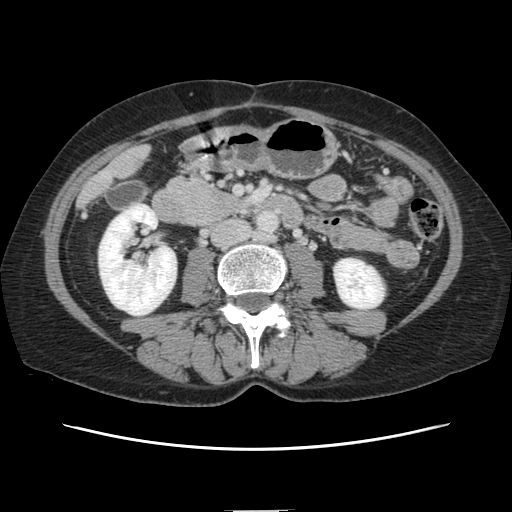
Contrast-enhanced abdominal CT, one axial slice. Slice 29 of 141 in the series (ordered by position). 120 kVp. Intravenous contrast given. Soft-tissue window (W 400 / L 40 HU). 2.5 mm slice thickness. 512 × 512 image matrix. Female patient, age 63 years. Case-level facts recorded for this patient, not image findings: diagnosis: colorectal cancer liver metastases, imaged before liver resection; multiple liver metastases: yes; largest metastasis: 3.2 cm; chemotherapy before resection: yes.
Outlined on this slice (outlined manually by an expert reader):
- liver: bounding box [x1, y1, x2, y2] px = [82, 147, 148, 202]